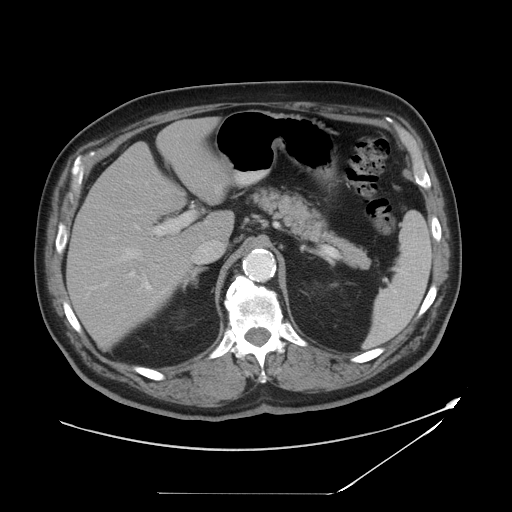
Contrast-enhanced abdominal CT, one axial slice; slice 29 of 49 in the series (ordered by position); 120 kVp; intravenous contrast given; soft-tissue window (W 400 / L 40 HU); 5 mm slice thickness; 512 × 512 image matrix, field of view 461 × 461 mm. Male patient, age 72 years. From the clinical record (not read from this slice): diagnosis: colorectal cancer liver metastases, imaged before liver resection; multiple liver metastases: no.
Annotated regions visible in this slice (outlined manually by an expert reader):
- hepatic veins: bounding box <96,181,148,268> (left, top, right, bottom; pixels)
- liver: <67,120,232,344>
- planned liver remnant (the part of the liver to remain after resection): <67,168,192,344>
- portal vein (with intrahepatic branches): <91,212,193,291>
- liver metastasis: <211,183,223,201>